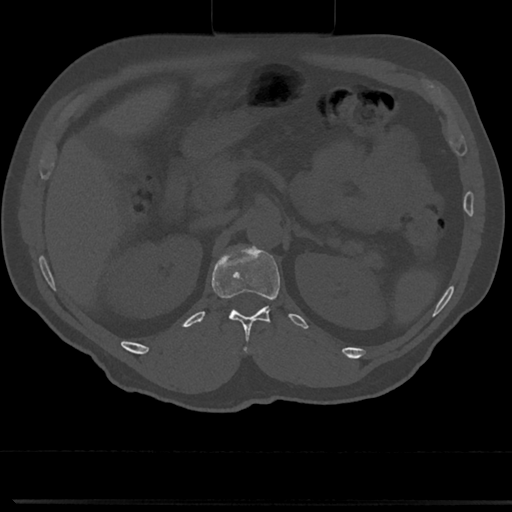
CT including the spine, one axial slice; slice 134 of 817 in the series (ordered by position); reconstruction kernel Br40s/3; bone window (W 1800 / L 400 HU); 0.5 mm slice thickness; 512 × 512 image matrix. Patient: male, 61 years. From the clinical record (not read from this slice): primary cancer: prostate.
Outlined on this slice (semi-automatic segmentation, software-assisted and operator-edited):
- T12 vertebra: bounding box <214,262,282,357> (left, top, right, bottom; pixels)